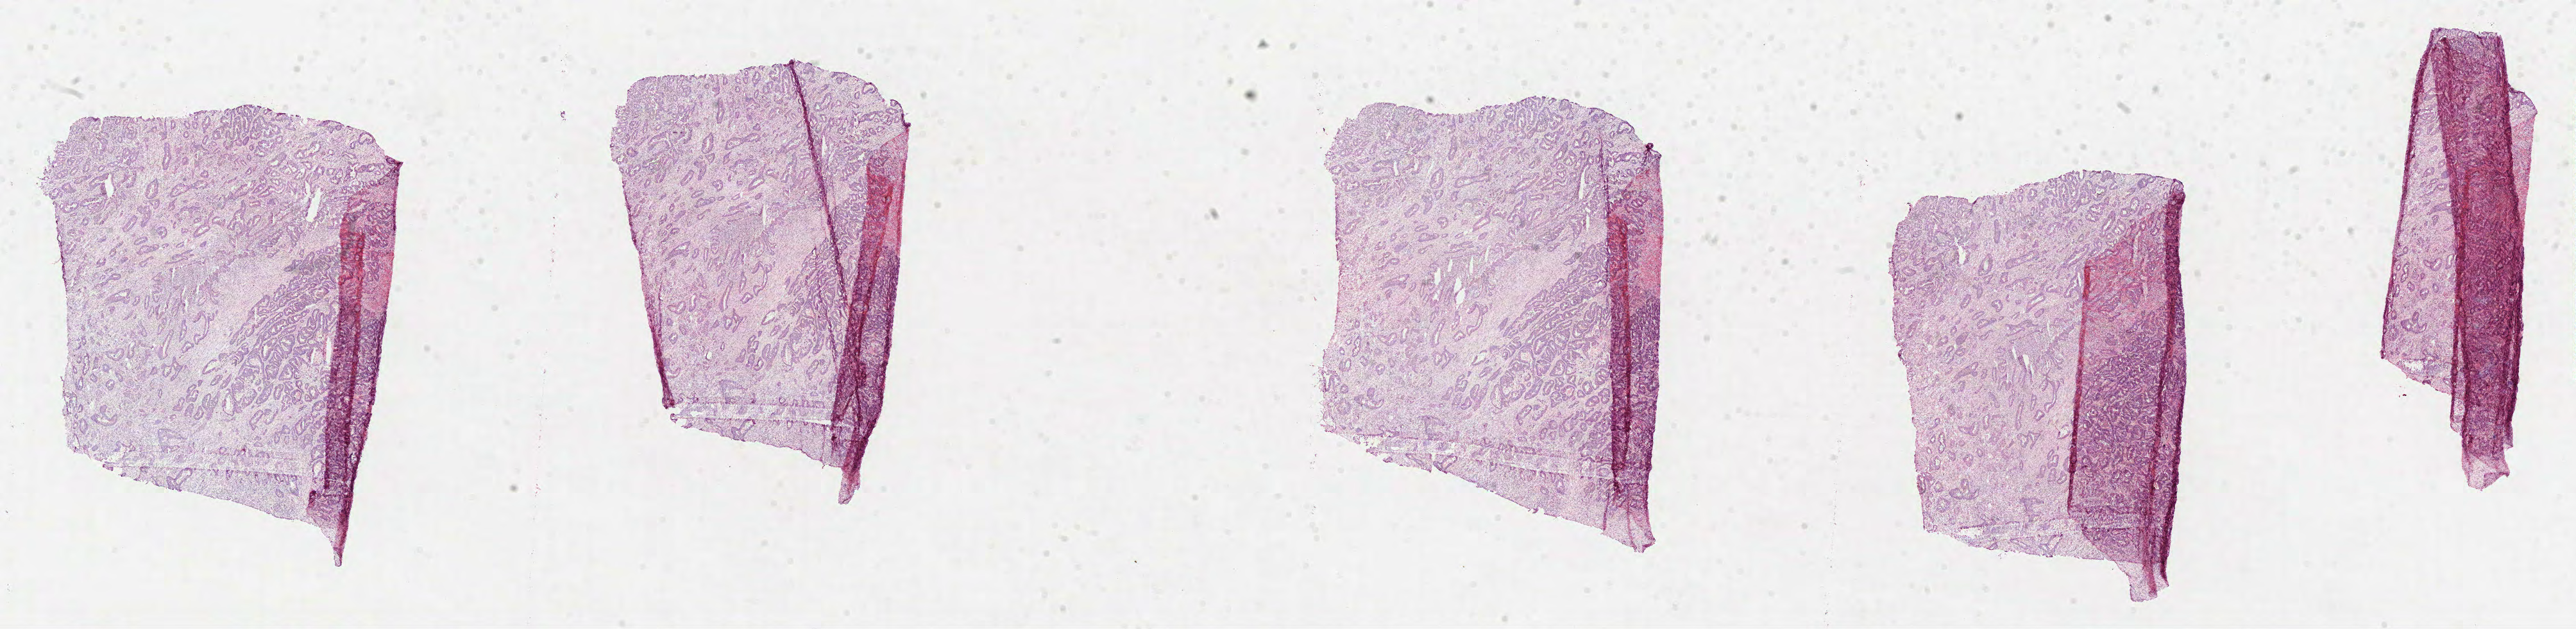
Digitized Hematoxylin and eosin (H&E) stained tissue section (whole slide), low-resolution overview of the scanned area, about 32.4 x 7.9 mm (acquisition: 40x scan); formalin-fixed paraffin-embedded (FFPE) diagnostic section; sample: primary tumour, colon. Male, age 65 years at initial diagnosis.
* histologic diagnosis: Adenocarcinoma, NOS (sigmoid colon)
* AJCC pathologic stage: IIIB (7th edition)
* lymph nodes positive (case pathology): 3 of 34 examined
* TNM: T4a N1 M0